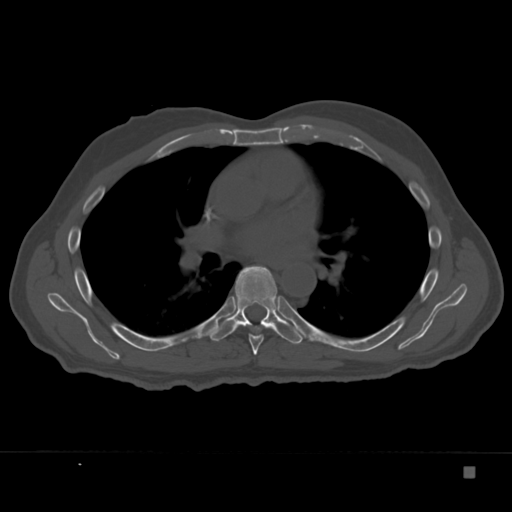
CT including the spine, one axial slice; slice 230 of 332 in the series (ordered by position); reconstruction kernel Br40s; 120 kVp; bone window (W 1800 / L 400 HU); 1.5 mm slice thickness; 512 × 512 image matrix, field of view 389 × 389 mm. Male patient, age 72 years. Case-level facts recorded for this patient, not image findings: primary cancer: skeletal.
Outlined on this slice (semi-automatically segmented with operator editing):
- T6 vertebra: box from (x=248, y=334) to (x=264, y=355) px
- T7 vertebra: (x=210, y=266)–(x=307, y=344)